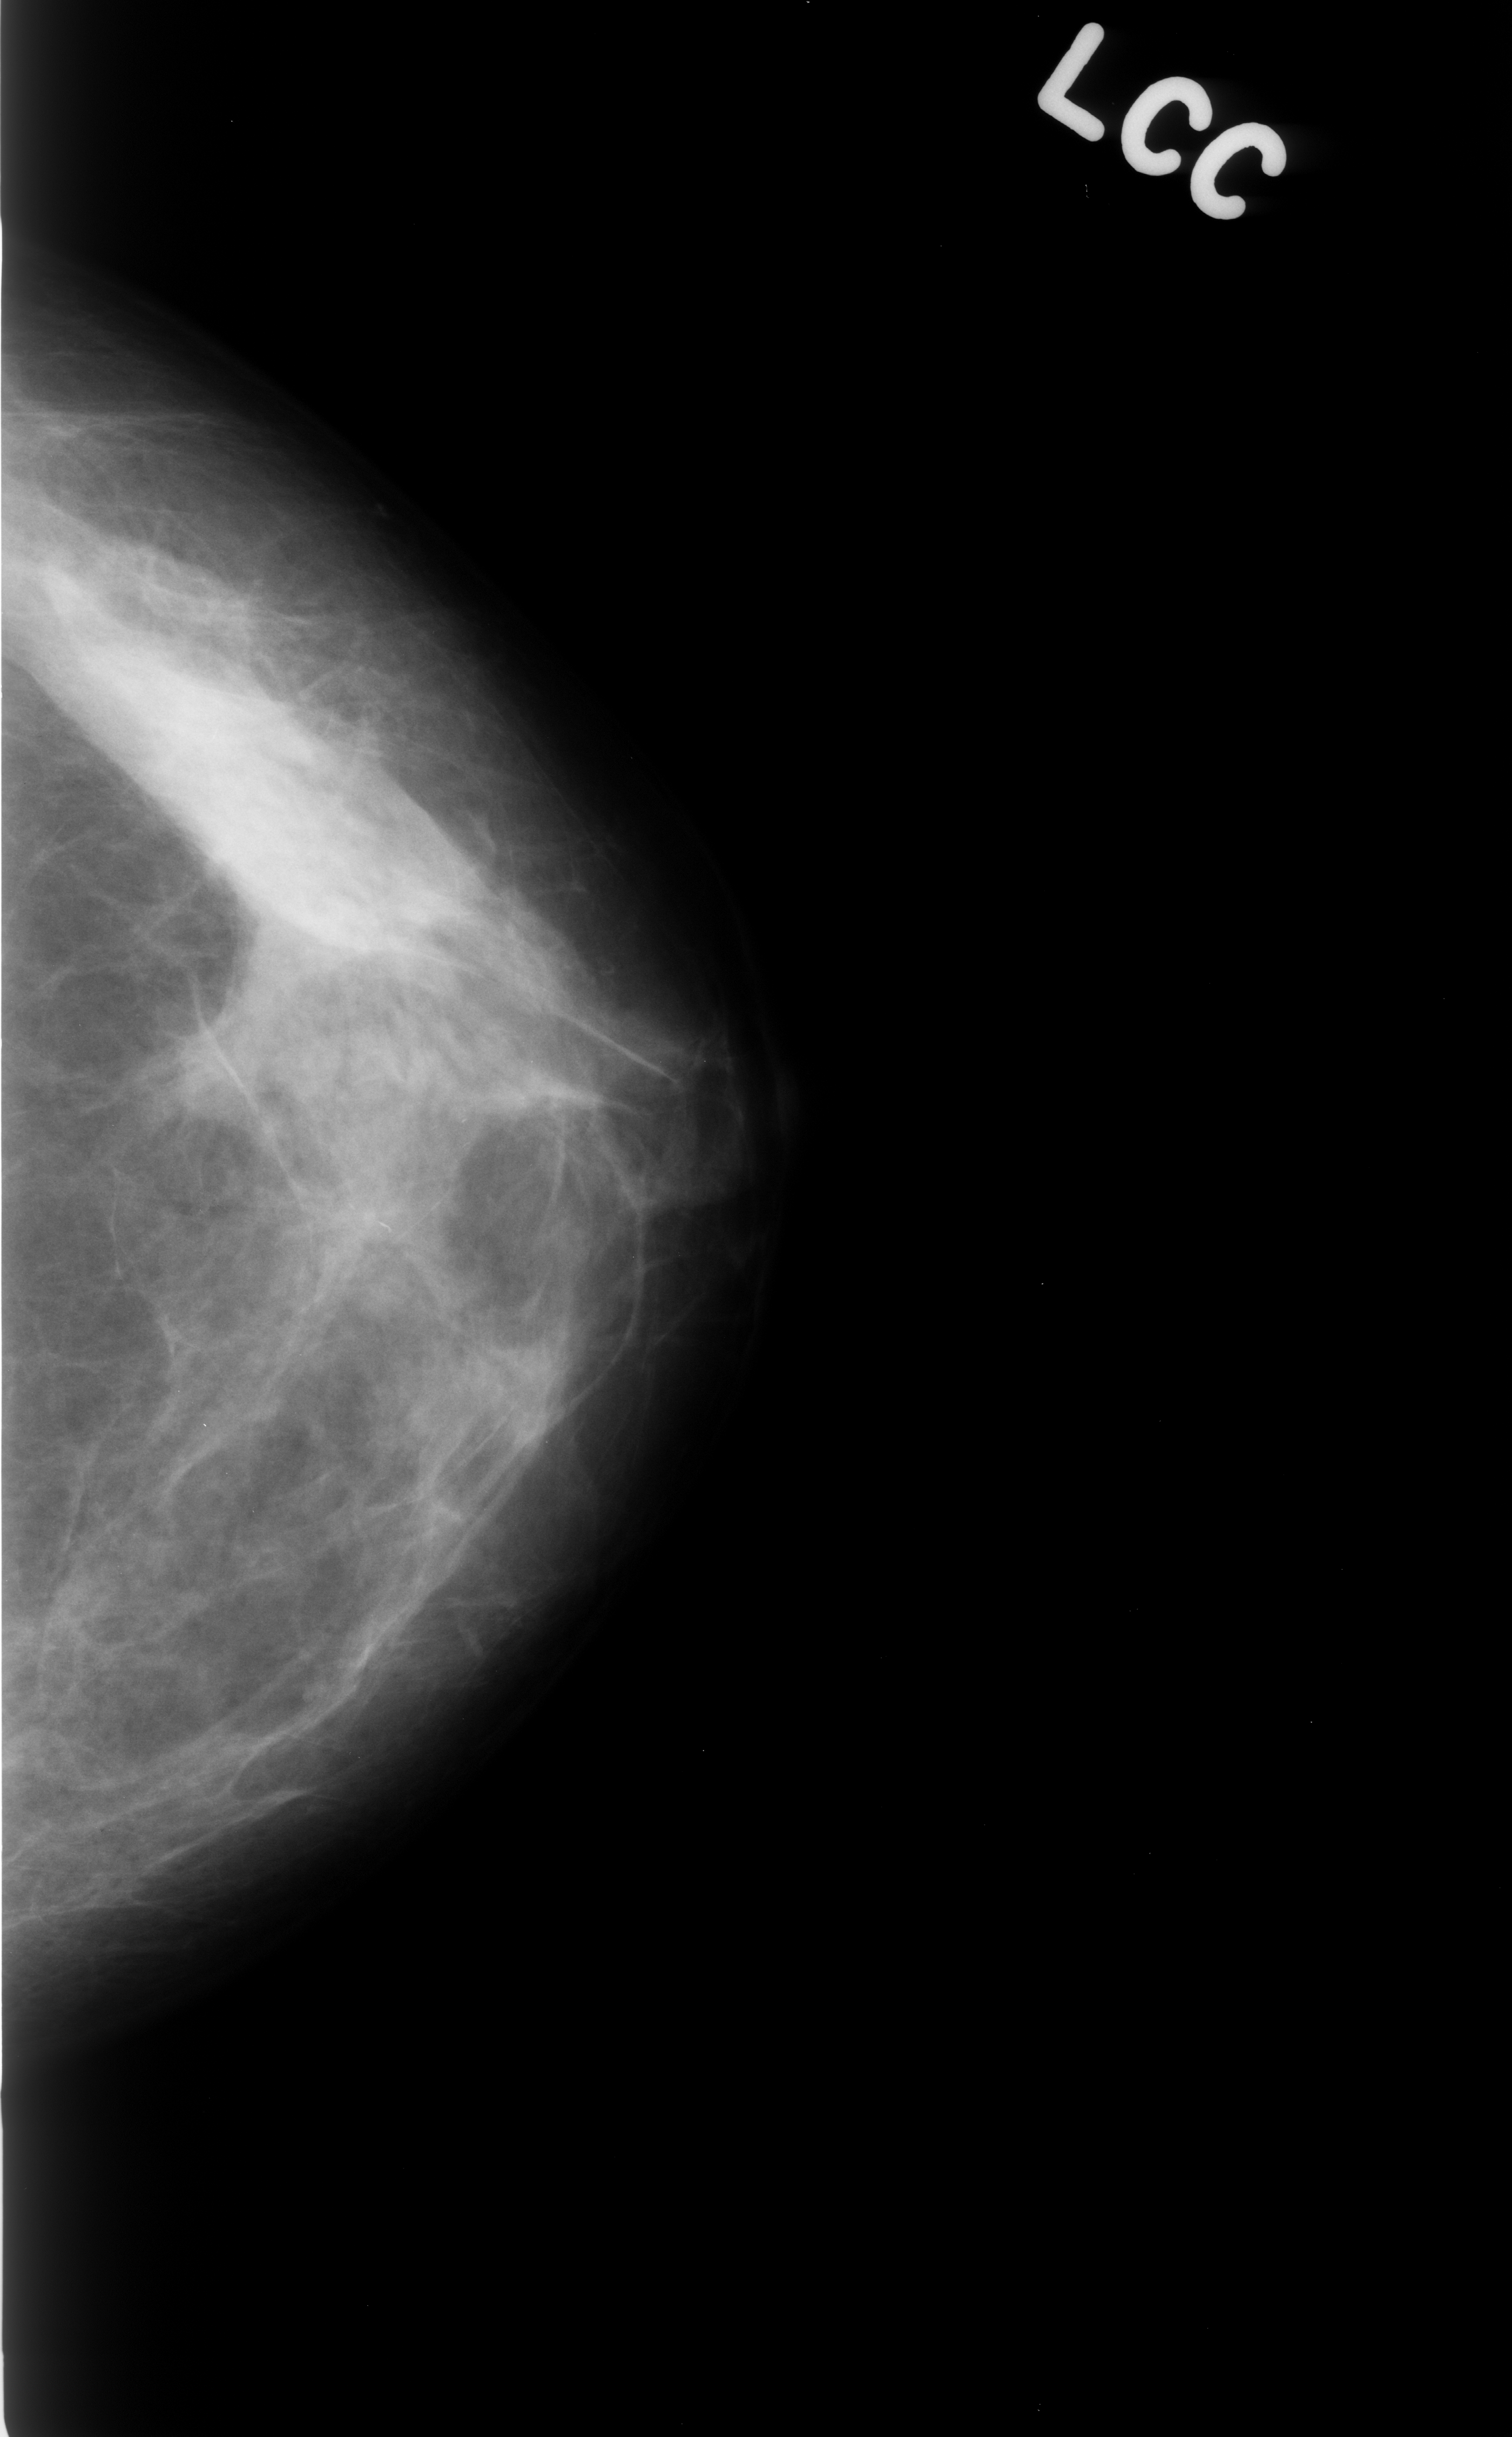
Scanned film-screen mammogram; left breast; CC view; BI-RADS breast density category 2 (scale 1–4).
Abnormality record for this image: Finding 1 of 2: calcifications, morphology fine linear branching, distribution linear; BI-RADS assessment category 4; subtlety rating 4 on a 1 (subtle) to 5 (obvious) scale; pathology result (as recorded, not read from the image): benign. Finding 2 of 2: calcifications, morphology fine linear branching, distribution linear; BI-RADS assessment category 4; subtlety rating 4 on a 1 (subtle) to 5 (obvious) scale; pathology (as recorded): benign.